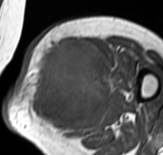
MRI of an extremity soft-tissue mass, one axial slice; position 39 of 65 along the scan axis; MR volume resampled by the dataset authors to the PET/CT grid (not the native acquisition matrix); 3.27 mm slice thickness; 163 × 155 image matrix. Female patient. From the clinical record (not read from this slice): histological type: pleomorphic leiomyosarcoma; grade: high; site of the primary tumour: left thigh.
Outlined on this slice (expert contour drawn on MRI and transferred to this co-registered scan by the dataset authors):
- gross tumour volume including surrounding oedema: bounding box <32,38,109,134> (left, top, right, bottom; pixels)
- gross tumour volume (mass): <35,38,107,125>